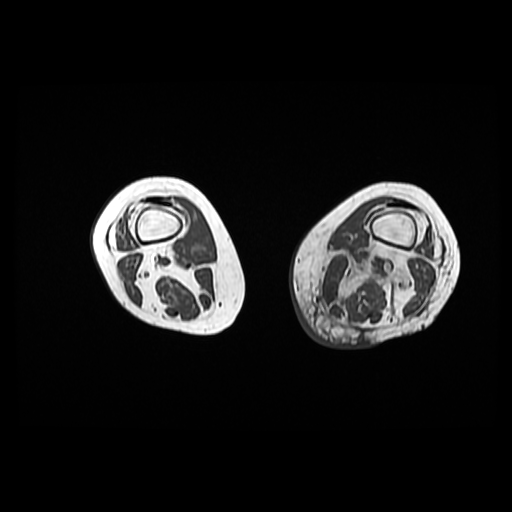
MRI of an extremity soft-tissue mass, one axial slice; position 18 of 42 along the scan axis; 6 mm slice thickness; 512 × 512 image matrix. Female patient. From the clinical record (not read from this slice): histological type: pleomorphic leiomyosarcoma; grade: high; site of the primary tumour: left thigh.
Outlined on this slice (manually delineated by an expert):
- gross tumour volume including surrounding oedema: box from (x=316, y=247) to (x=411, y=321) px